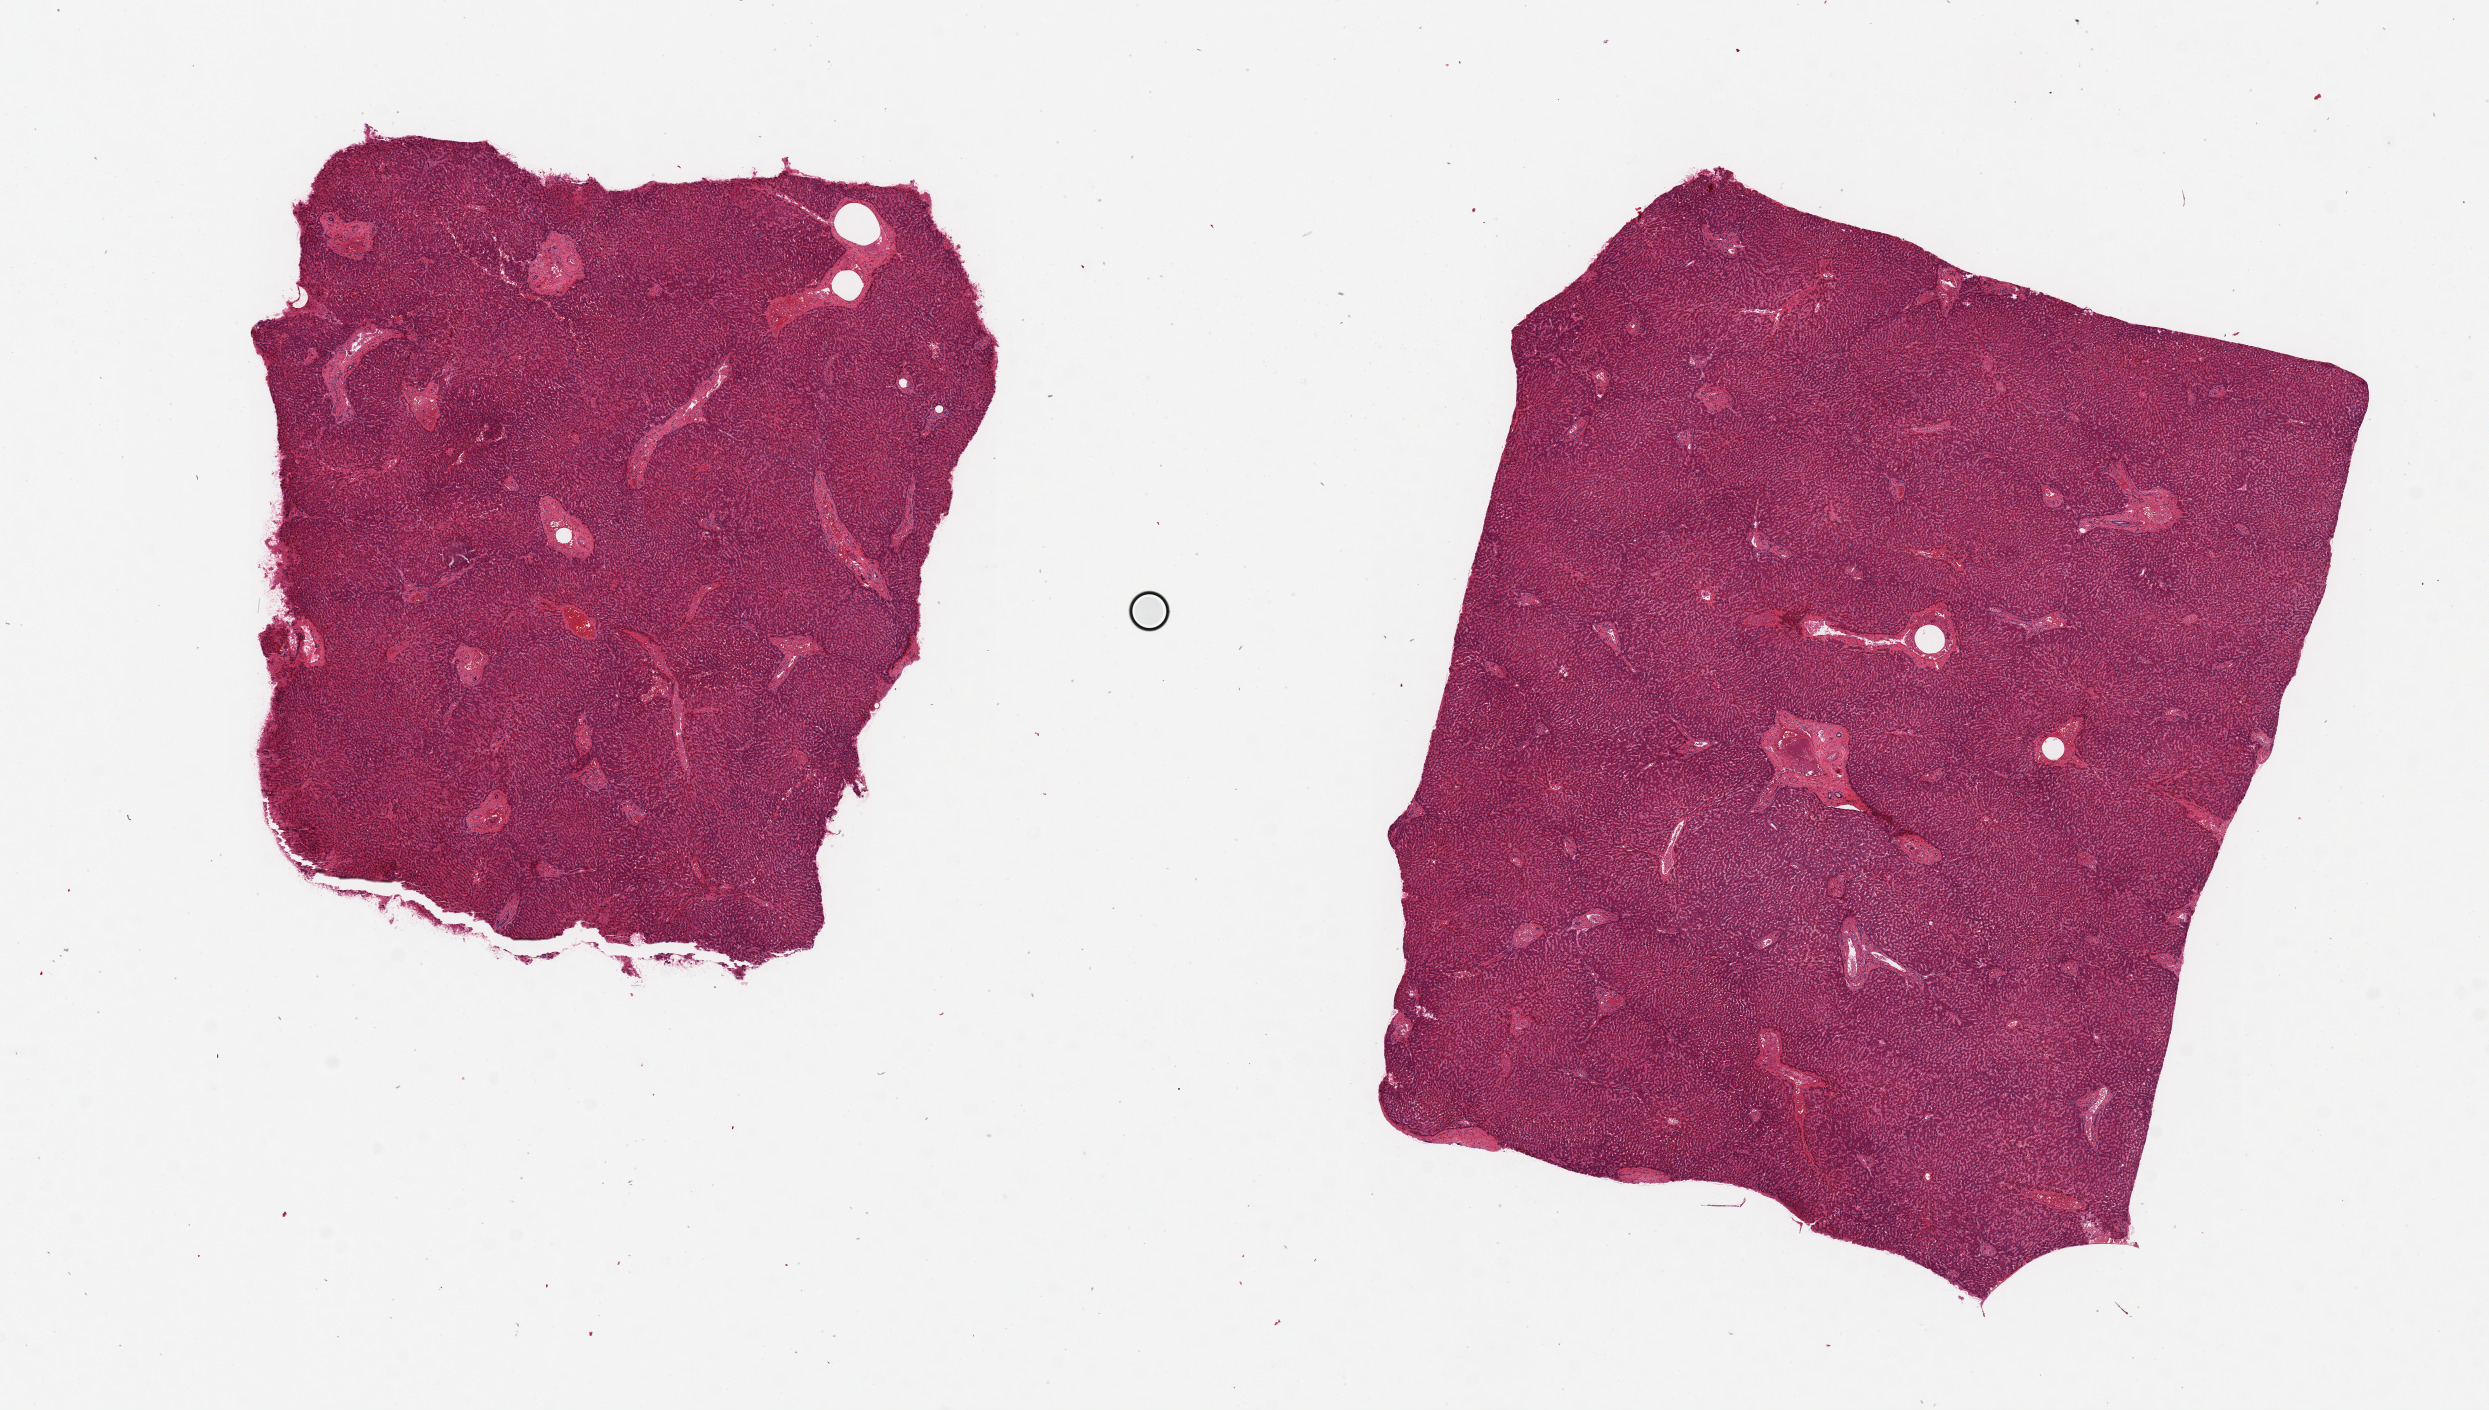
Whole-slide image, haematoxylin and eosin stain, whole scanned area (about 19.7 x 11.2 mm) shown as a low-resolution overview. PAXgene-fixed paraffin-embedded (PFPE) section. Section of liver (target tissue). Tissue donor sample. Donor sex: male.
* review note (as recorded): 2 pieces, 8x7 & 6x6mm; no fat, fibrosis or excess congestion